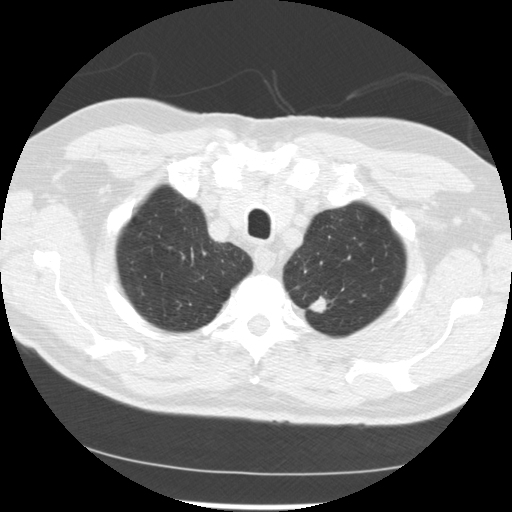
Low-dose screening chest CT, one axial slice. Slice 216 of 249 in the series (ordered by position). Reconstruction kernel STANDARD. 120 kVp. Lung window (W 1500 / L -600 HU). 2.5 mm slice thickness. 512 × 512 image matrix, field of view 341 × 341 mm.
Structures marked on this image (expert manual segmentation):
- lesion 2 (tumor, upper lobe of left lung): bounding box (x1, y1, x2, y2) in pixels: (310, 297, 327, 313)